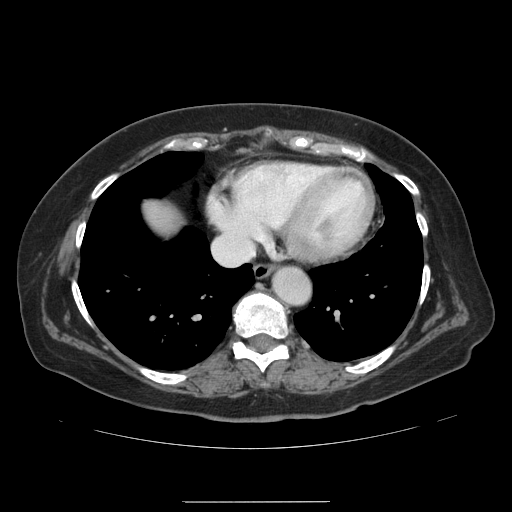
Contrast-enhanced abdominal CT, one axial slice. Position 131 of 141 along the scan axis. Intravenous contrast given. Soft-tissue window (W 400 / L 40 HU). 2.5 mm slice thickness. 512 × 512 image matrix. Female patient, age 74 years. Case-level facts recorded for this patient, not image findings: diagnosis: colorectal cancer liver metastases, imaged before liver resection; multiple liver metastases: yes; largest metastasis: 7 cm; disease in both lobes: yes.
Structures marked on this image (expert manual segmentation):
- liver: bounding box <147,206,173,228> (left, top, right, bottom; pixels)
- planned liver remnant (the part of the liver to remain after resection): <147,208,158,226>